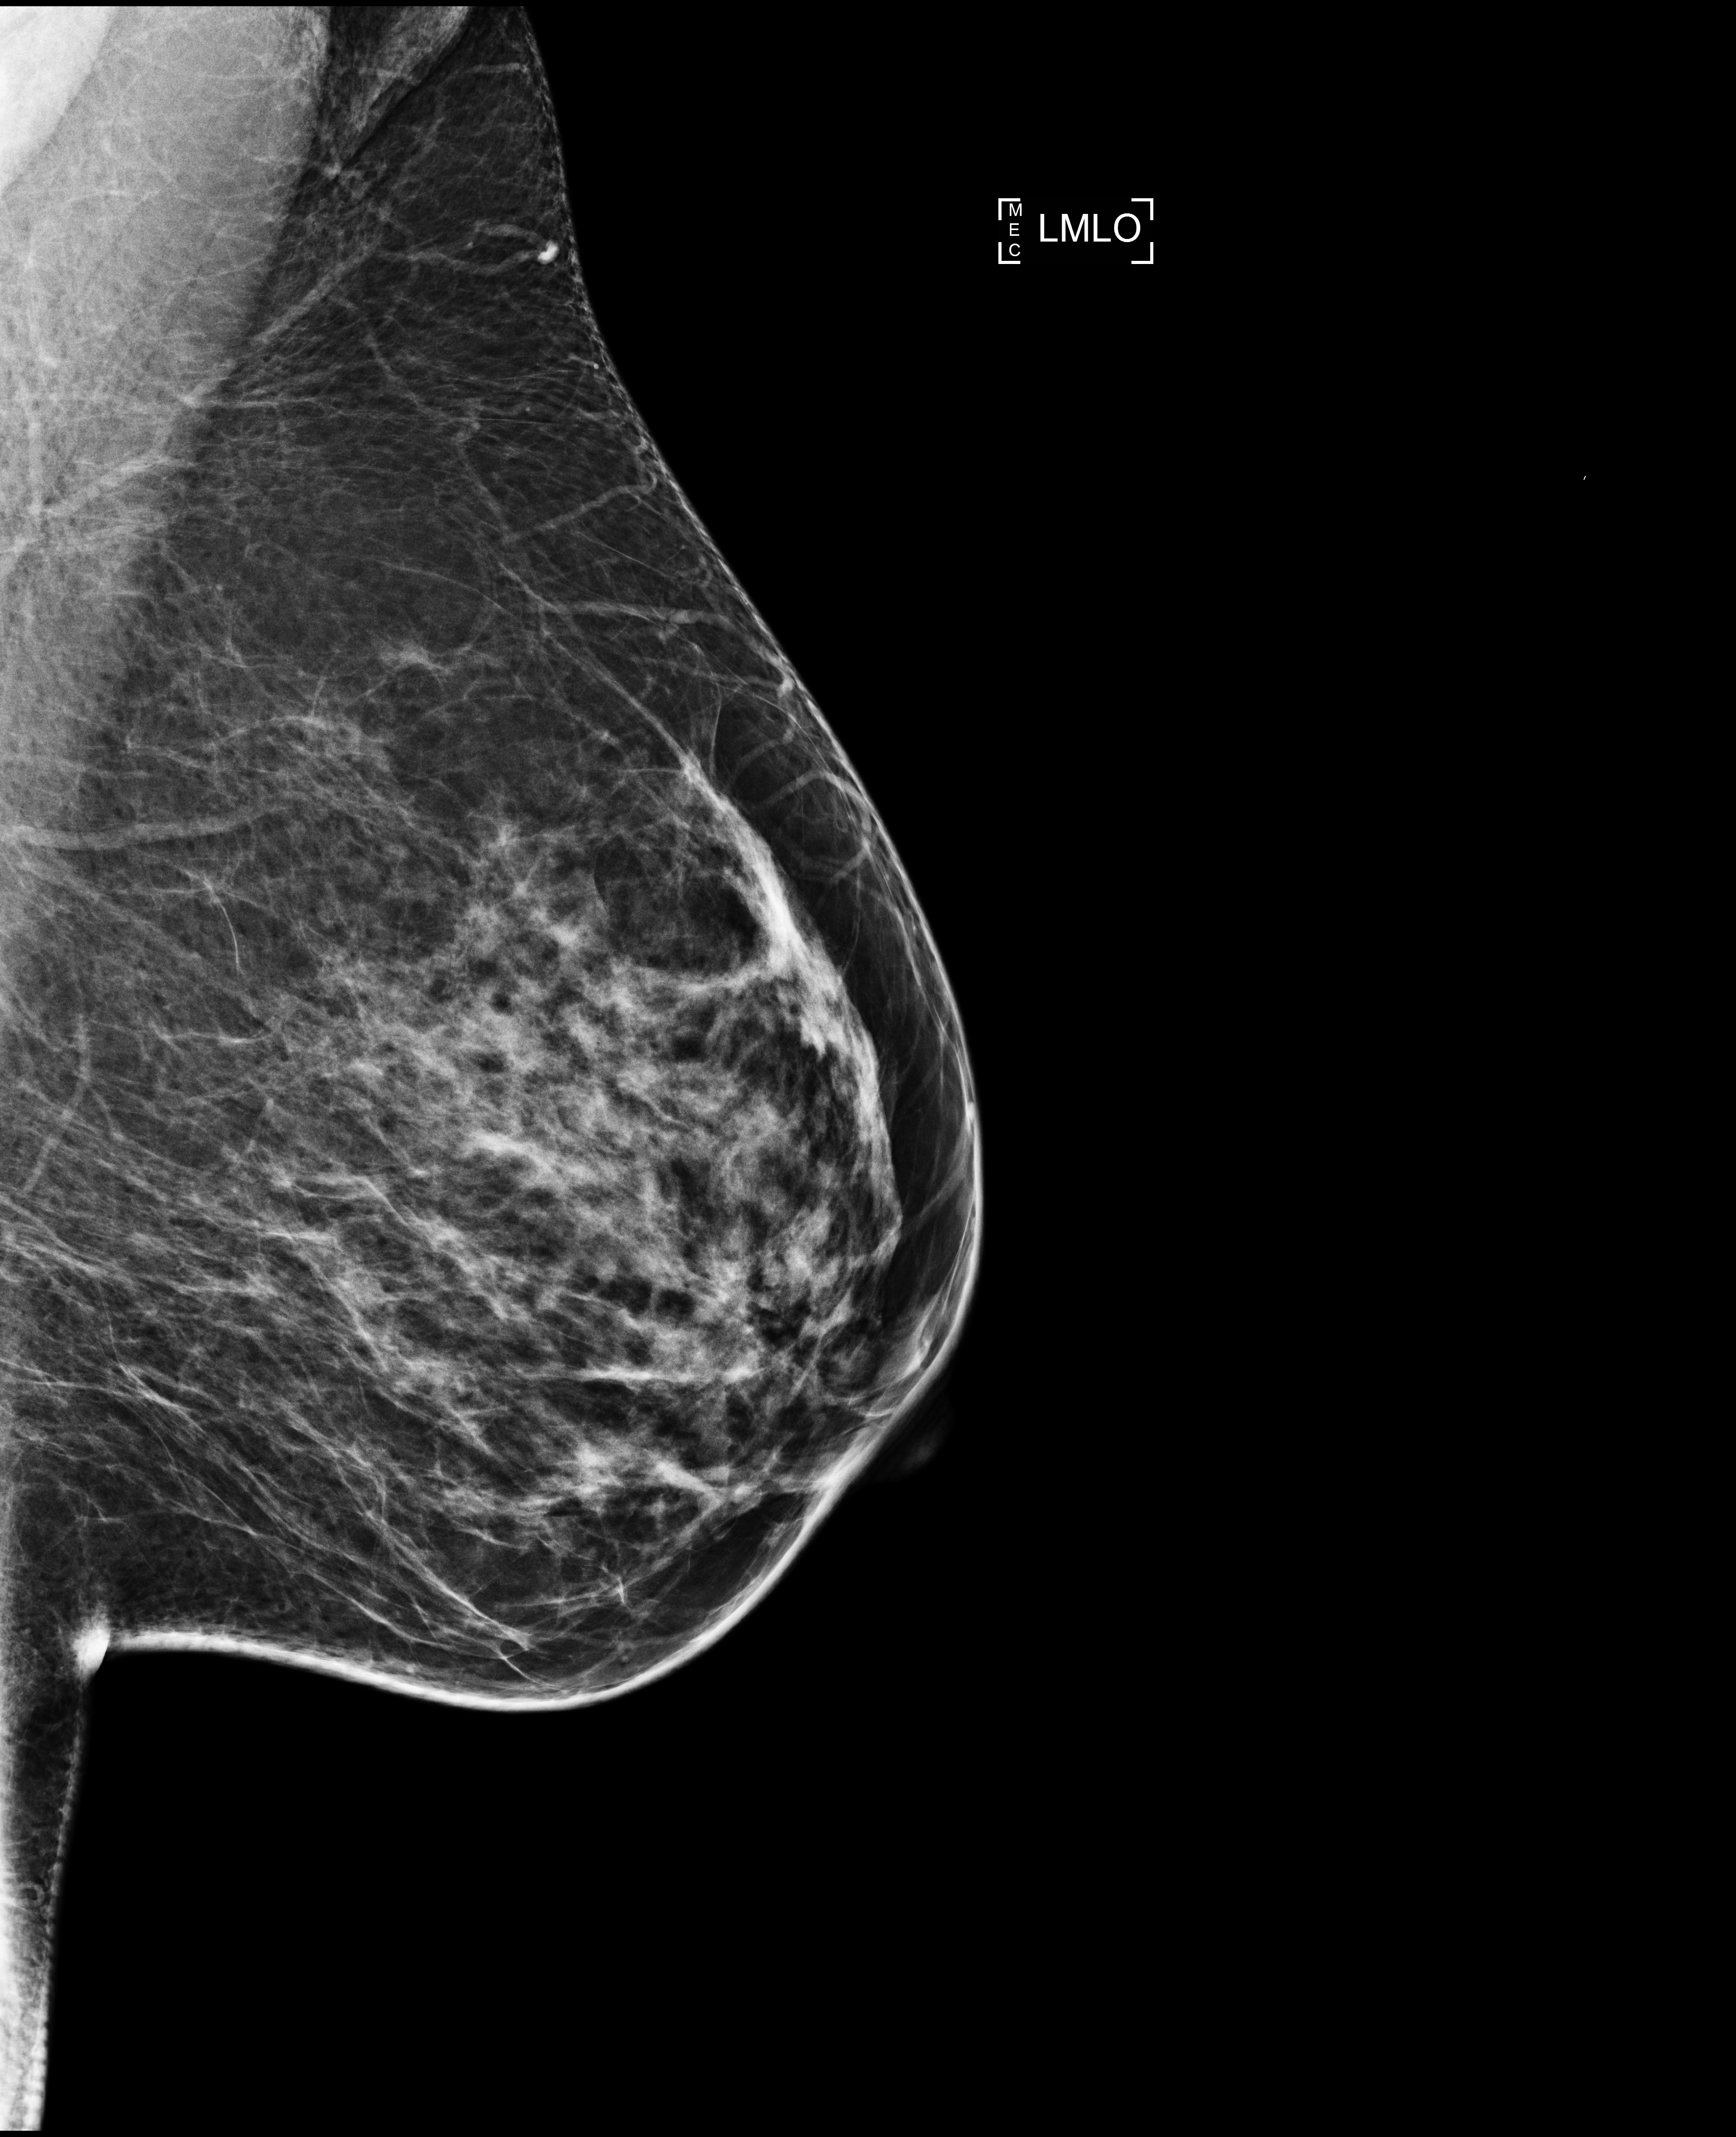
Digital mammogram (FFDM); left breast; mediolateral oblique (MLO) view; screening examination; compressed breast thickness 64 mm; system: Selenia Dimensions. Patient aged 46 years (female).
Breast density at the screening exam (both breasts): heterogeneously dense (BI-RADS density category c). Final BI-RADS category for the screening round (tomosynthesis exam, both breasts): category 1. Recall: no recall after this screen.